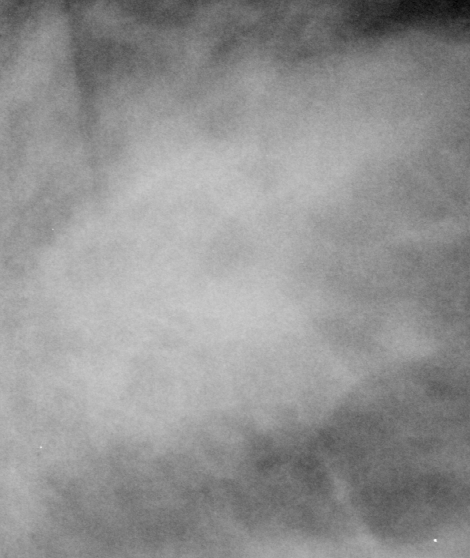
Crop from a digitized film mammogram around one marked abnormality; left breast; CC view.
Mass, shape irregular, margins ill defined; BI-RADS assessment category 4; subtlety rating 4 on a 1 (subtle) to 5 (obvious) scale; pathology result (as recorded, not read from the image): malignant.